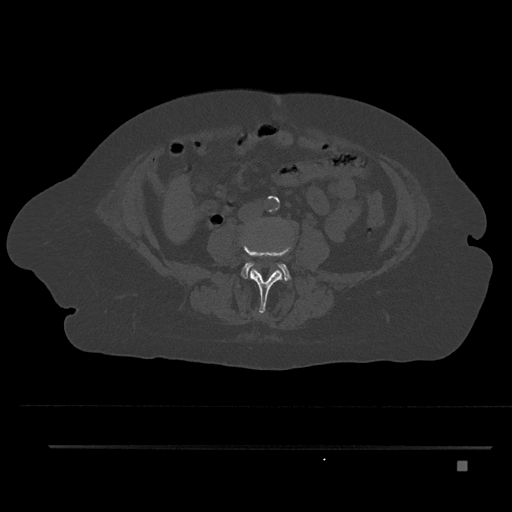
CT including the spine, one axial slice; position 111 of 797 along the scan axis; reconstruction kernel Br40s/3; 120 kVp; bone window (W 1800 / L 400 HU); 0.5 mm slice thickness; 512 × 512 image matrix, field of view 437 × 437 mm. Female patient, age 76 years. Case-level facts recorded for this patient, not image findings: primary cancer: lung; vertebrae with lytic lesions (as recorded): T11, L3.
Outlined on this slice (semi-automatically segmented with operator editing):
- L3 vertebra: box from (x=242, y=242) to (x=292, y=313) px
- L4 vertebra: (x=241, y=236)–(x=290, y=281)